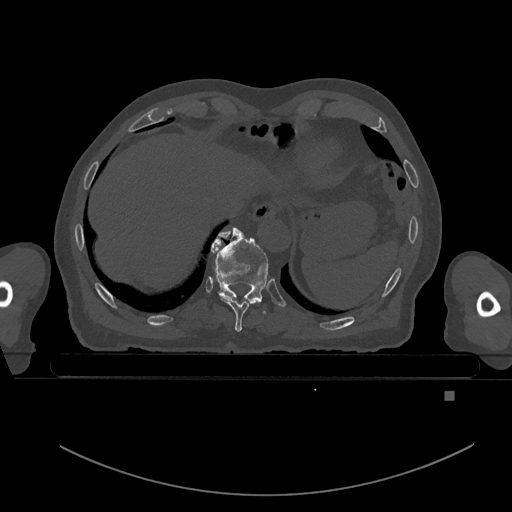
CT including the spine, one axial slice; slice 116 of 969 in the series (ordered by position); bone window (W 1800 / L 400 HU); 0.5 mm slice thickness; 512 × 512 image matrix, field of view 456 × 456 mm. Male patient, age 82 years. From the clinical record (not read from this slice): primary cancer: prostate.
Annotated regions visible in this slice (semi-automatic segmentation, software-assisted and operator-edited):
- T10 vertebra: bounding box (x1, y1, x2, y2) in pixels: (211, 227, 269, 302)
- T9 vertebra: (219, 231, 261, 332)